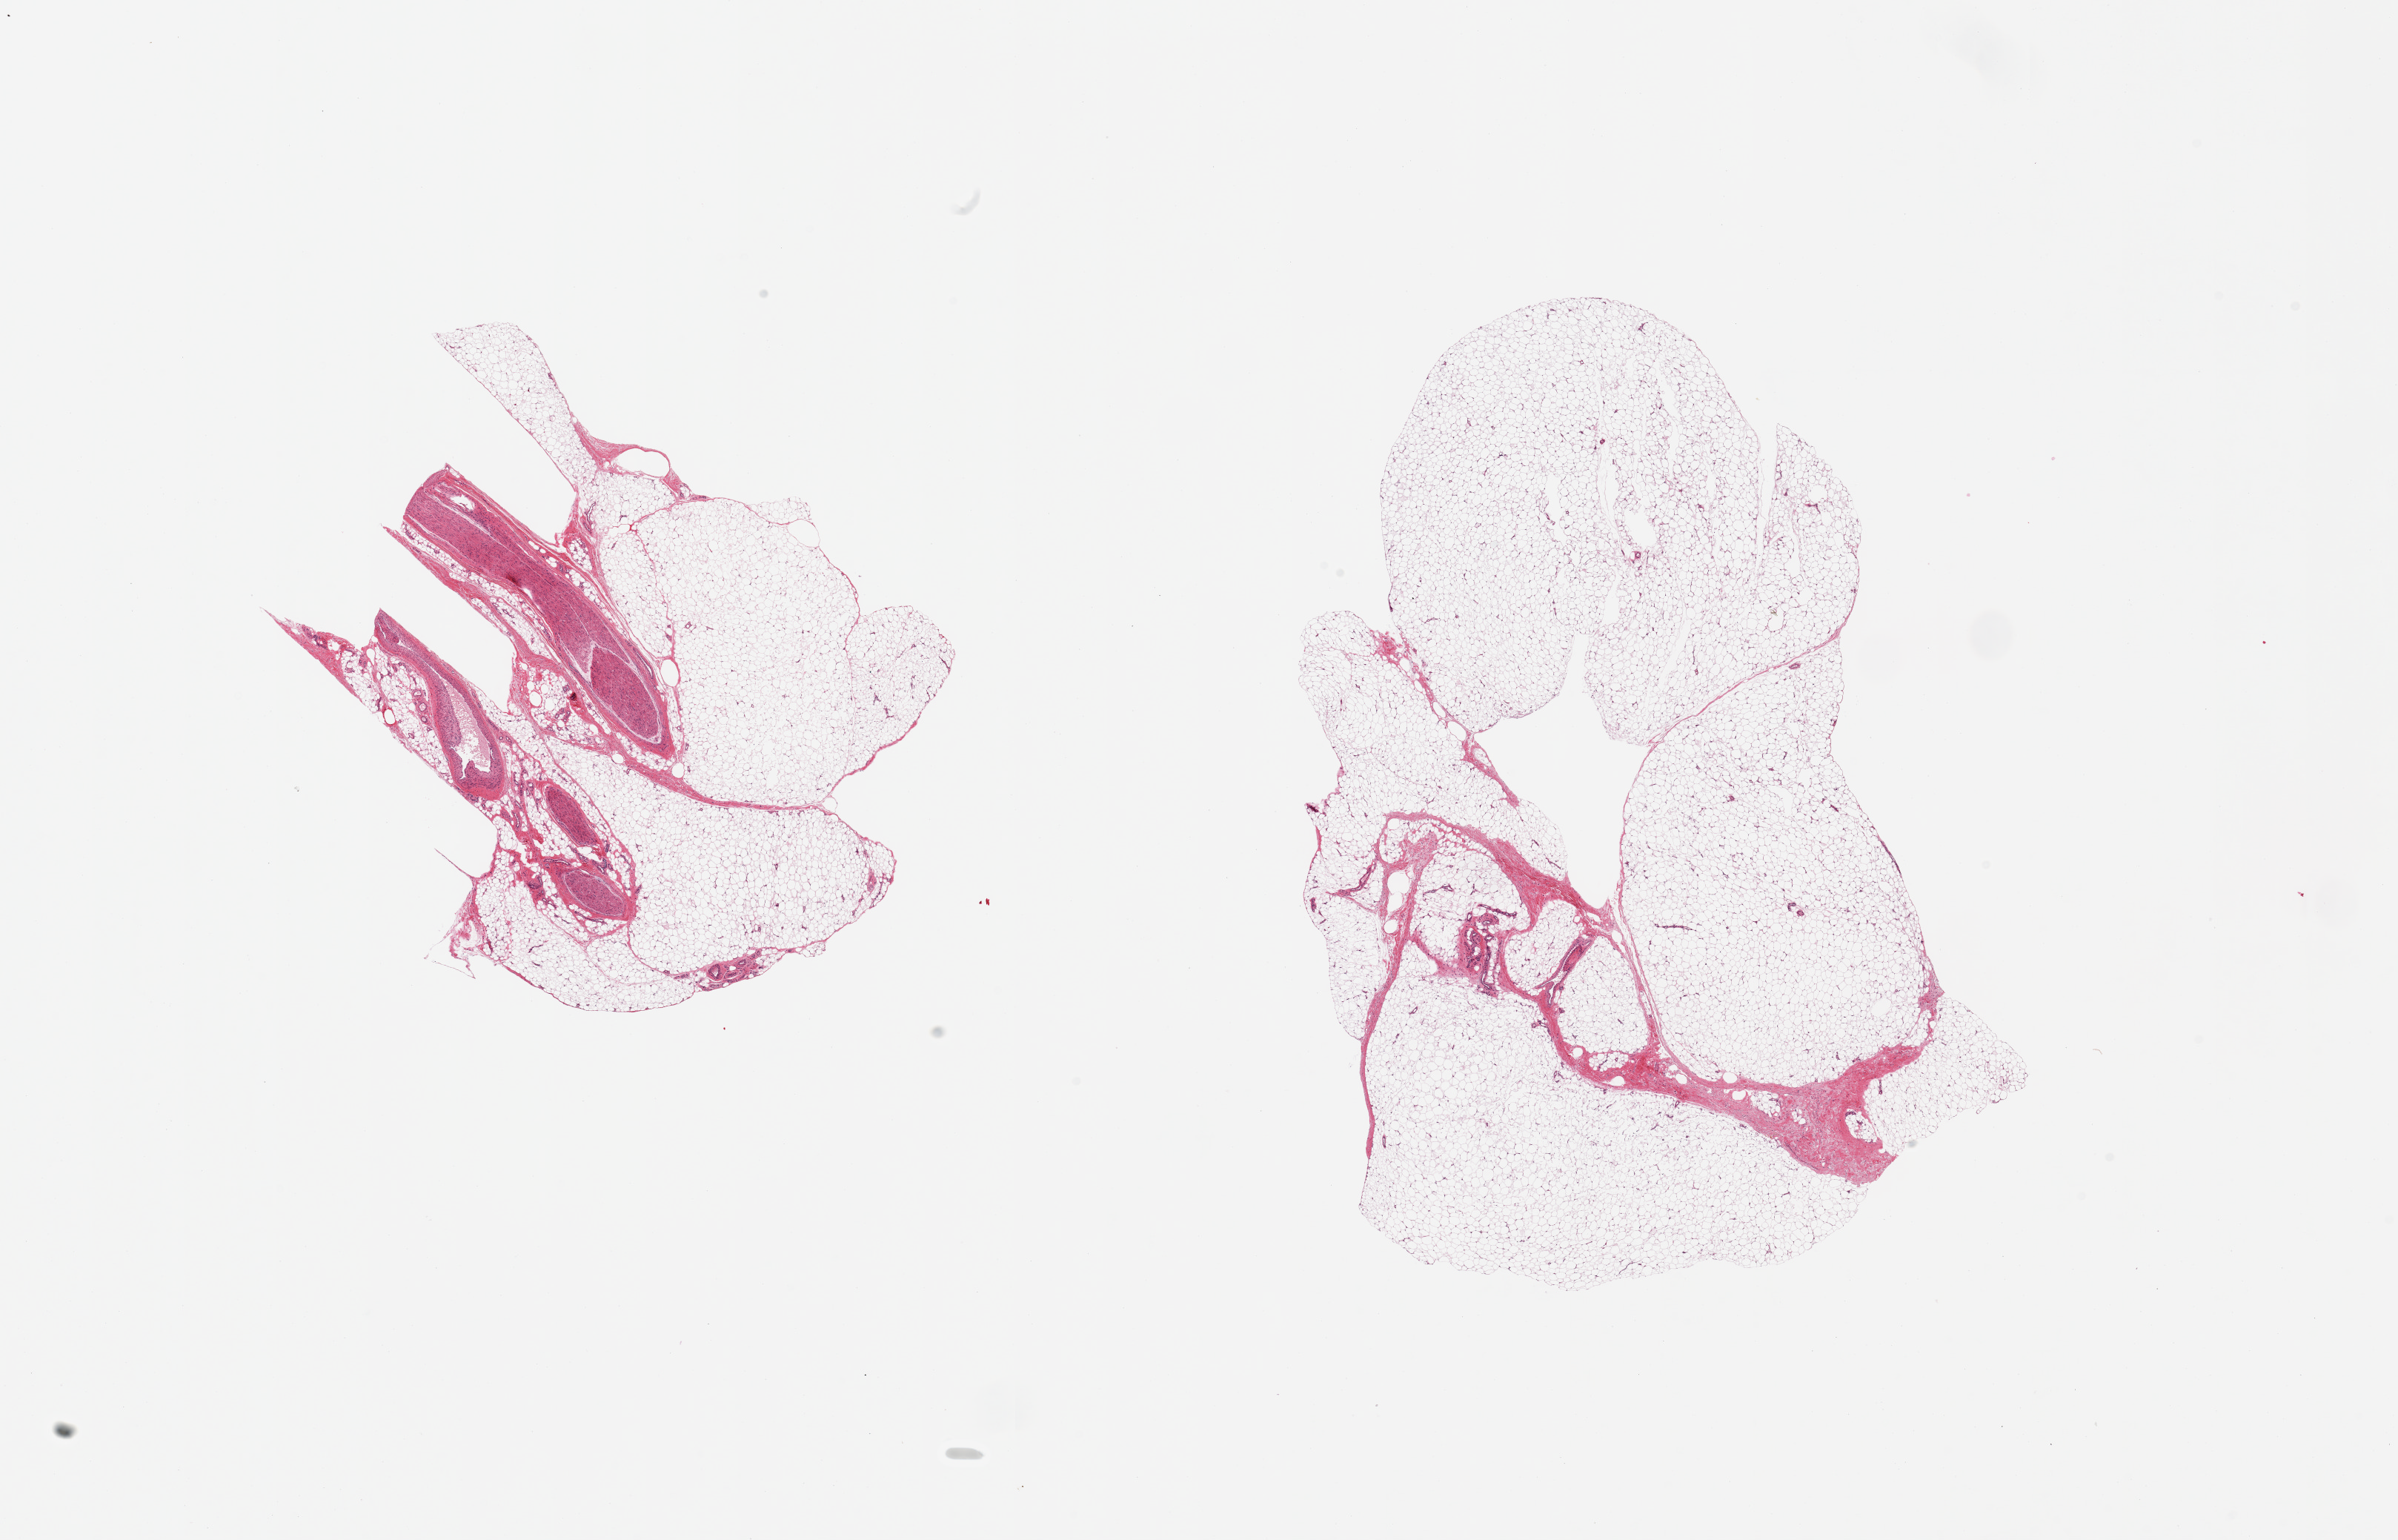
Digitized H&E-stained section, a low-resolution overview of the entire scanned area, about 25.6 x 16.4 mm, PAXgene-fixed, paraffin-embedded tissue, sampled site (target tissue): adipose tissue, tissue donor sample. Donor sex: male.
Review note (as recorded): 2 pieces; 1 with 20% stromal vascular content.